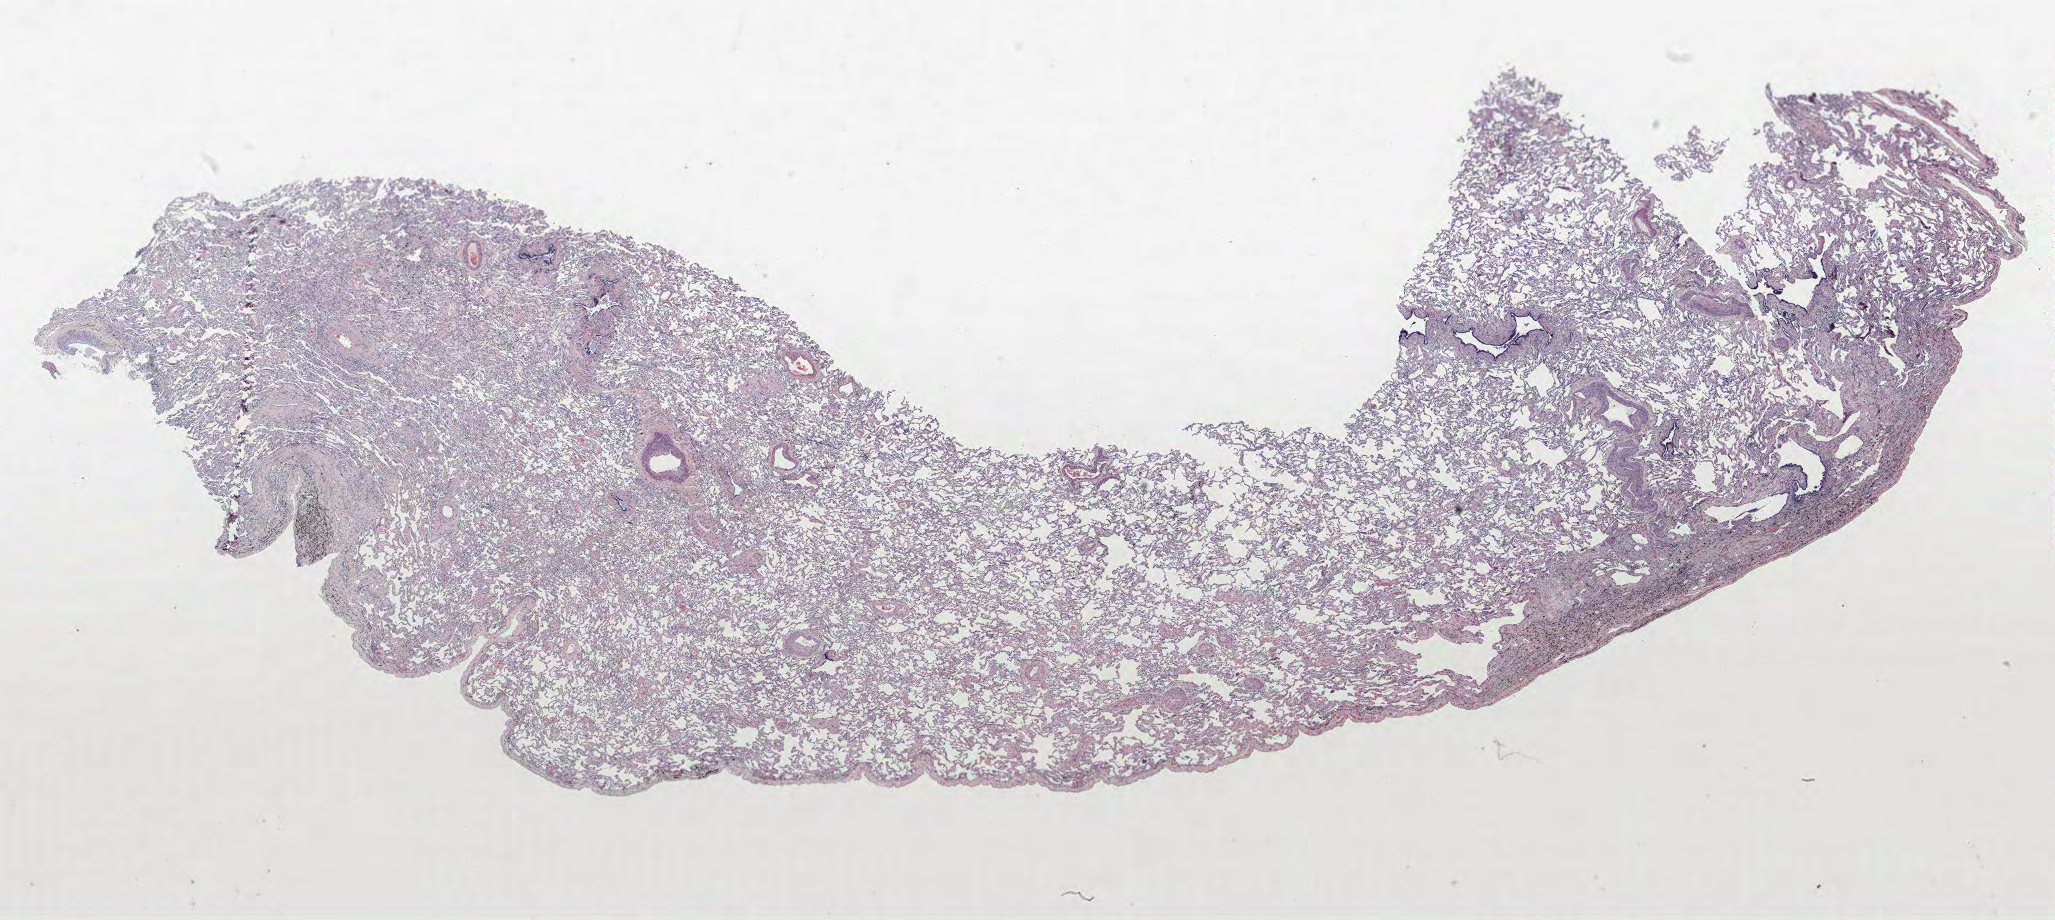
H&E whole-slide image, low-resolution overview of the scanned area, about 32.9 x 14.7 mm (slide scanned at 40x). FFPE section. Lung. Male, age 71 at enrolment. Former smoker at enrolment. Grade: moderately differentiated (G2).
- participant's lung-cancer diagnosis: Bronchiolo-alveolar adenocarcinoma, NOS
- primary tumour location (clinical record): right upper lobe
- tumour size (pathology): 25 mm
- stage (AJCC 6th edition): IIIA